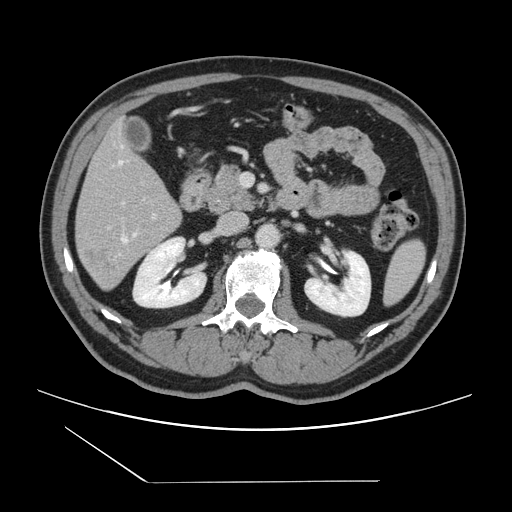
Contrast-enhanced abdominal CT, one axial slice; slice 62 of 157 in the series (ordered by position); intravenous contrast given; soft-tissue window (W 400 / L 40 HU); 2.5 mm slice thickness; 512 × 512 image matrix, field of view 407 × 407 mm. Male patient, age 61 years. Case-level facts recorded for this patient, not image findings: diagnosis: colorectal cancer liver metastases, imaged before liver resection; multiple liver metastases: yes; largest metastasis: 5.5 cm; chemotherapy before resection: no.
Annotated regions visible in this slice (expert manual segmentation):
- hepatic veins: bounding box (x1, y1, x2, y2) in pixels: (119, 160, 136, 242)
- liver: (76, 125, 181, 289)
- planned liver remnant (the part of the liver to remain after resection): (77, 124, 172, 218)
- portal vein (with intrahepatic branches): (108, 202, 156, 228)
- liver metastasis: (81, 246, 113, 281)